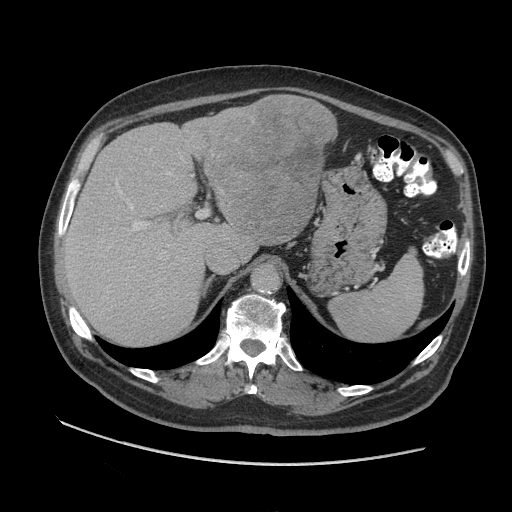
Contrast-enhanced abdominal CT (liver protocol), one axial slice. Position 64 of 109 along the scan axis. Reconstruction kernel STANDARD. 140 kVp. Soft-tissue window (W 400 / L 40 HU). 2.5 mm slice thickness. 512 × 512 image matrix, field of view 420 × 420 mm. Case-level facts recorded for this patient, not image findings: diagnosis: hepatocellular carcinoma (patient treated with transarterial chemoembolisation; whether this scan precedes or follows treatment is not stated here); TNM stage (as recorded): Stage-I; Child-Pugh class: A.
Annotated regions visible in this slice (semi-automatically segmented with operator editing):
- liver parenchyma outside the tumour (the mass and vessels are separate outlines, so this box may not span the whole liver): bounding box (x1, y1, x2, y2) in pixels: (64, 94, 324, 344)
- mass: (203, 94, 337, 245)
- liver vessels: (108, 172, 170, 248)